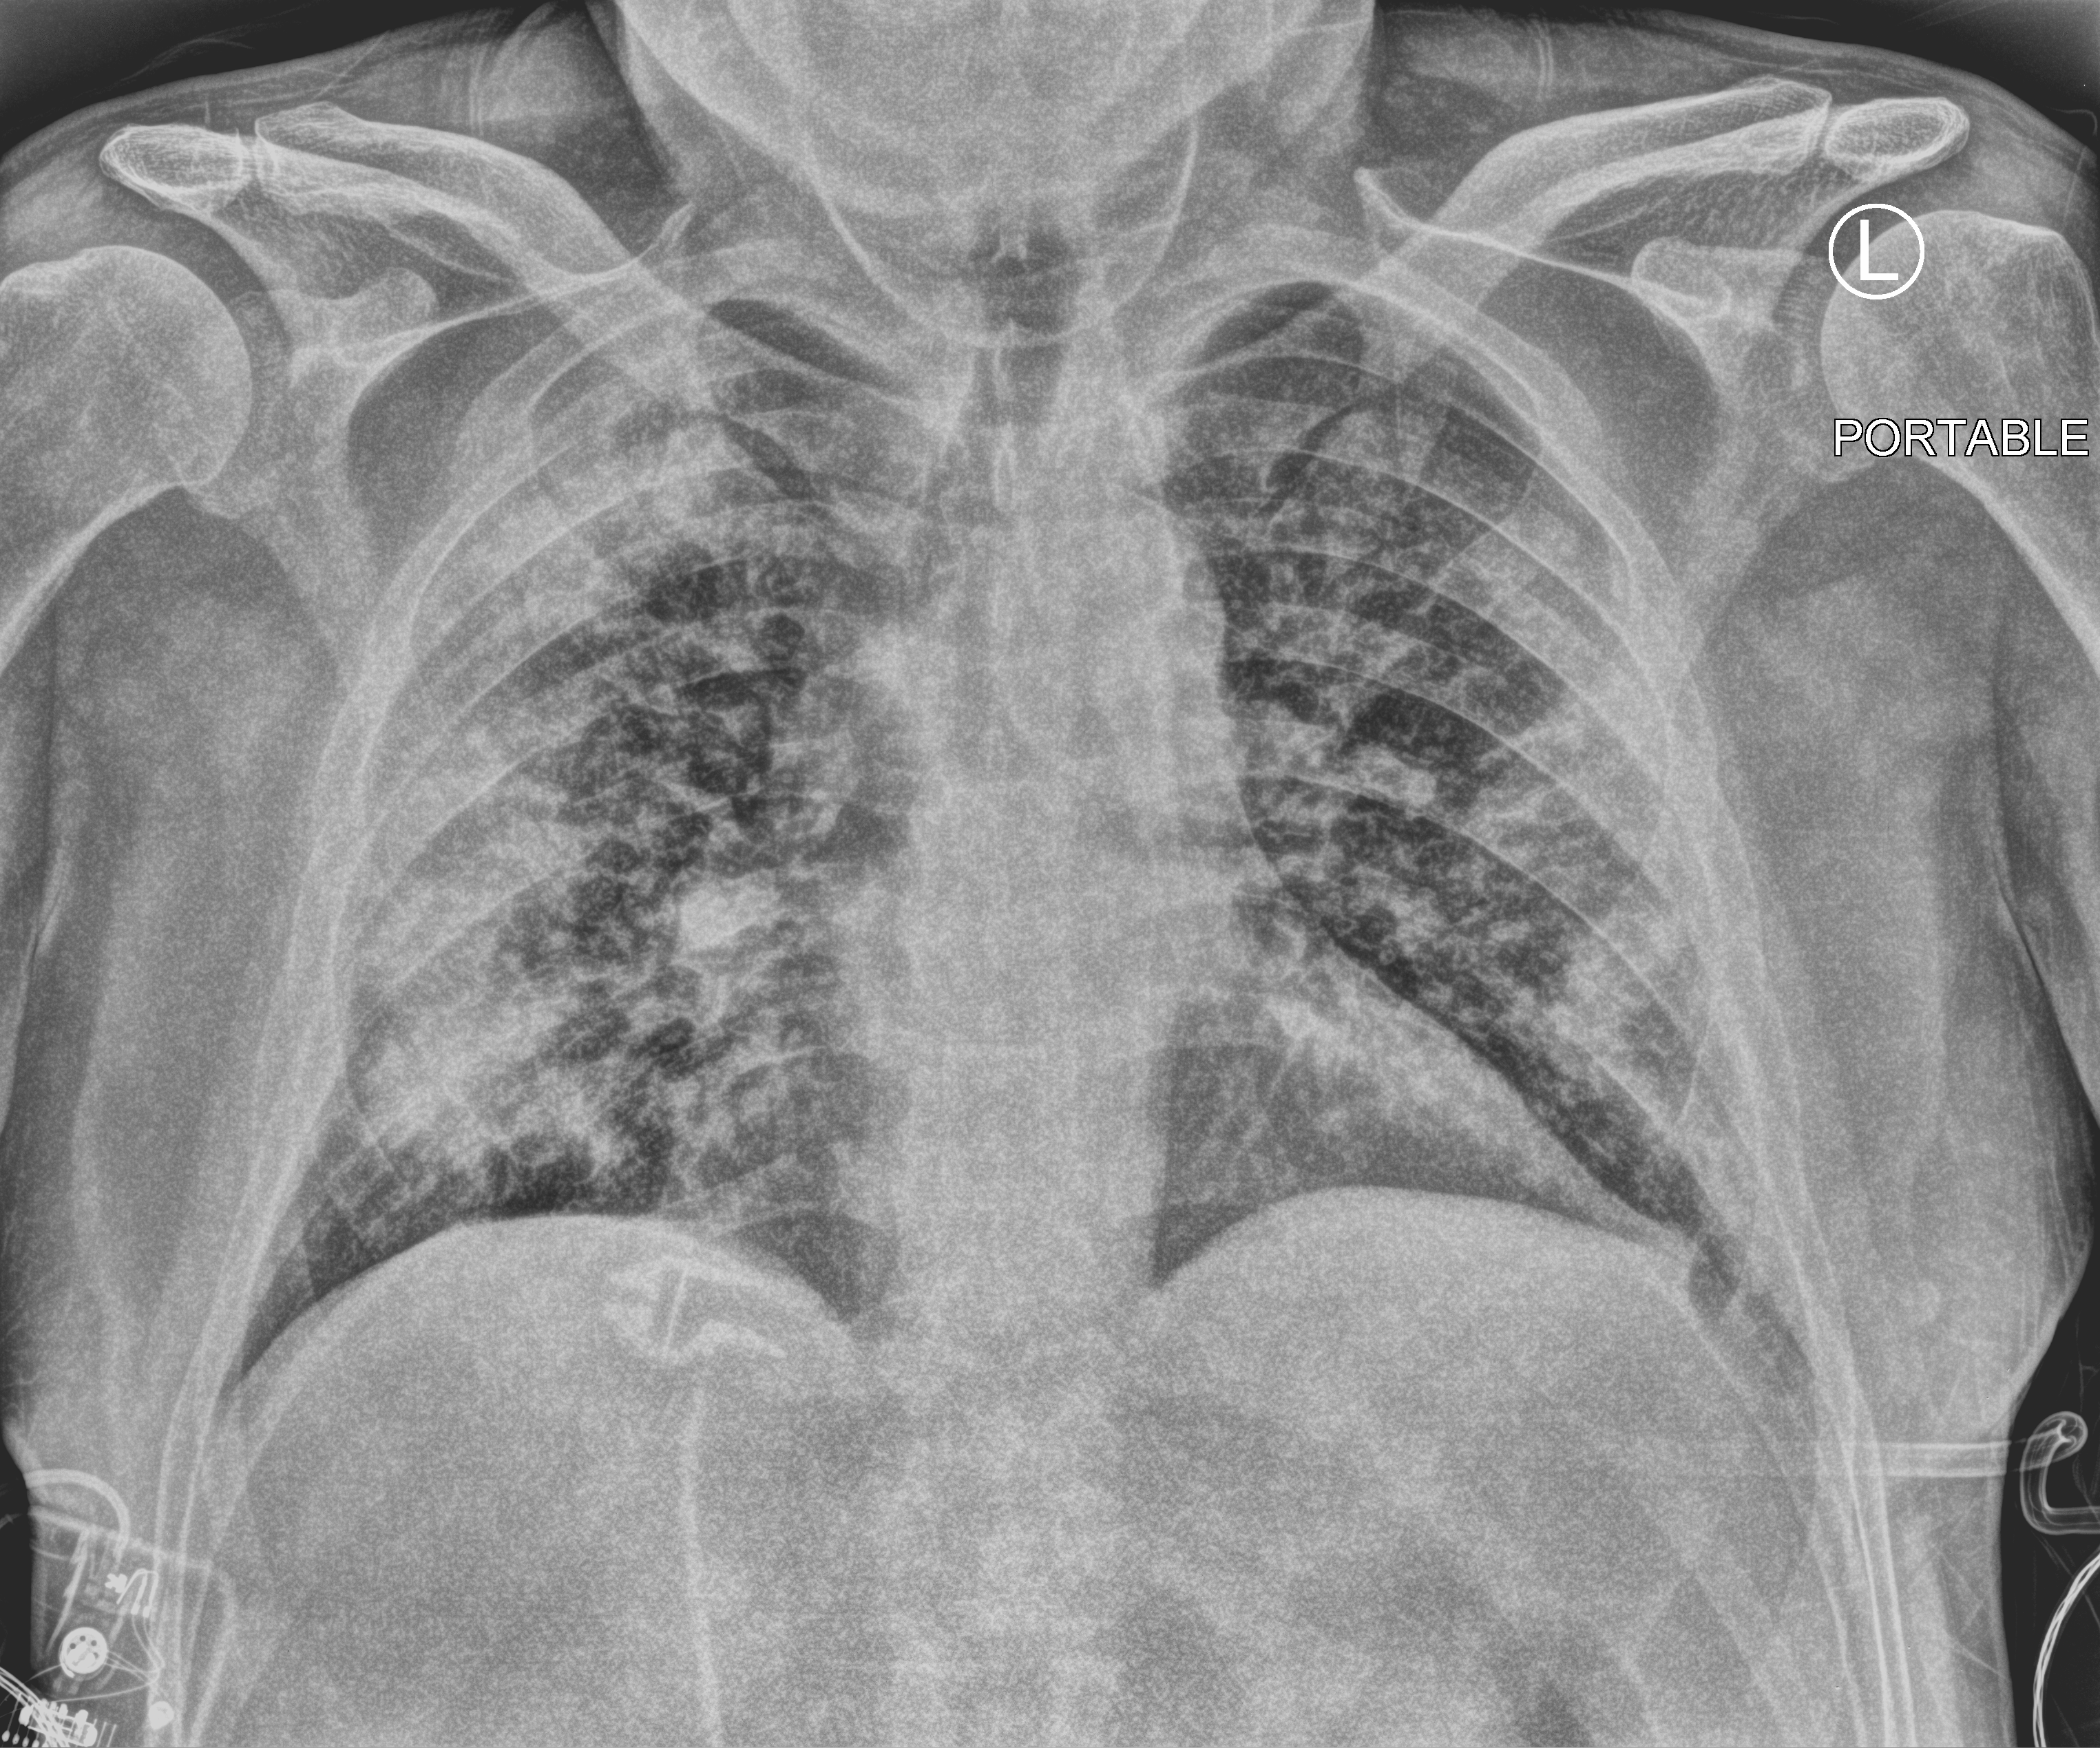
Portable chest radiograph. Male patient hospitalised with COVID-19, age 60–74 years.
Admission-level facts for this patient (not findings on this image; timing relative to this image not recorded): mechanically ventilated during this hospital stay: no; diabetes (admission record): no.